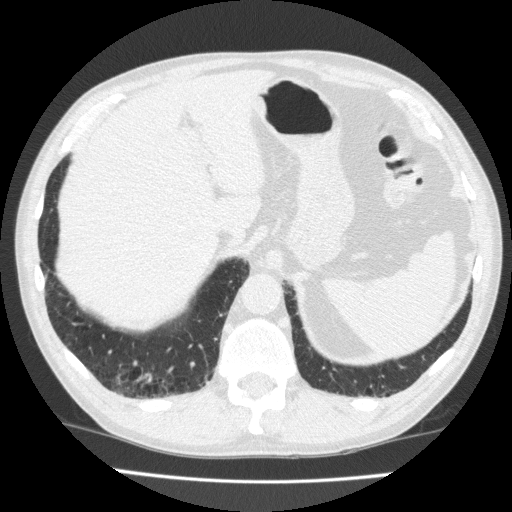
Axial slice from a low-dose chest CT screening exam, first (baseline) screen, lung window (W 1500 / L -600 HU), 2 mm slice thickness, standard (soft-tissue) reconstruction kernel (FC10), 120 kVp, 512 × 512 image matrix. Male, age 70 years at enrolment. Current smoker at enrolment.
Lesion marked by an expert reader, bounding box <116,360,167,400> (left, top, right, bottom; pixels). No non-calcified nodule or mass ≥4 mm was recorded by the screening reader at this exam. Participant outcome: lung cancer diagnosed 503 days after this screen (after the second annual screen) — squamous cell carcinoma, NOS, right lower lobe, moderately differentiated (G2), stage IA (AJCC 6th edition), 20 mm at pathology.